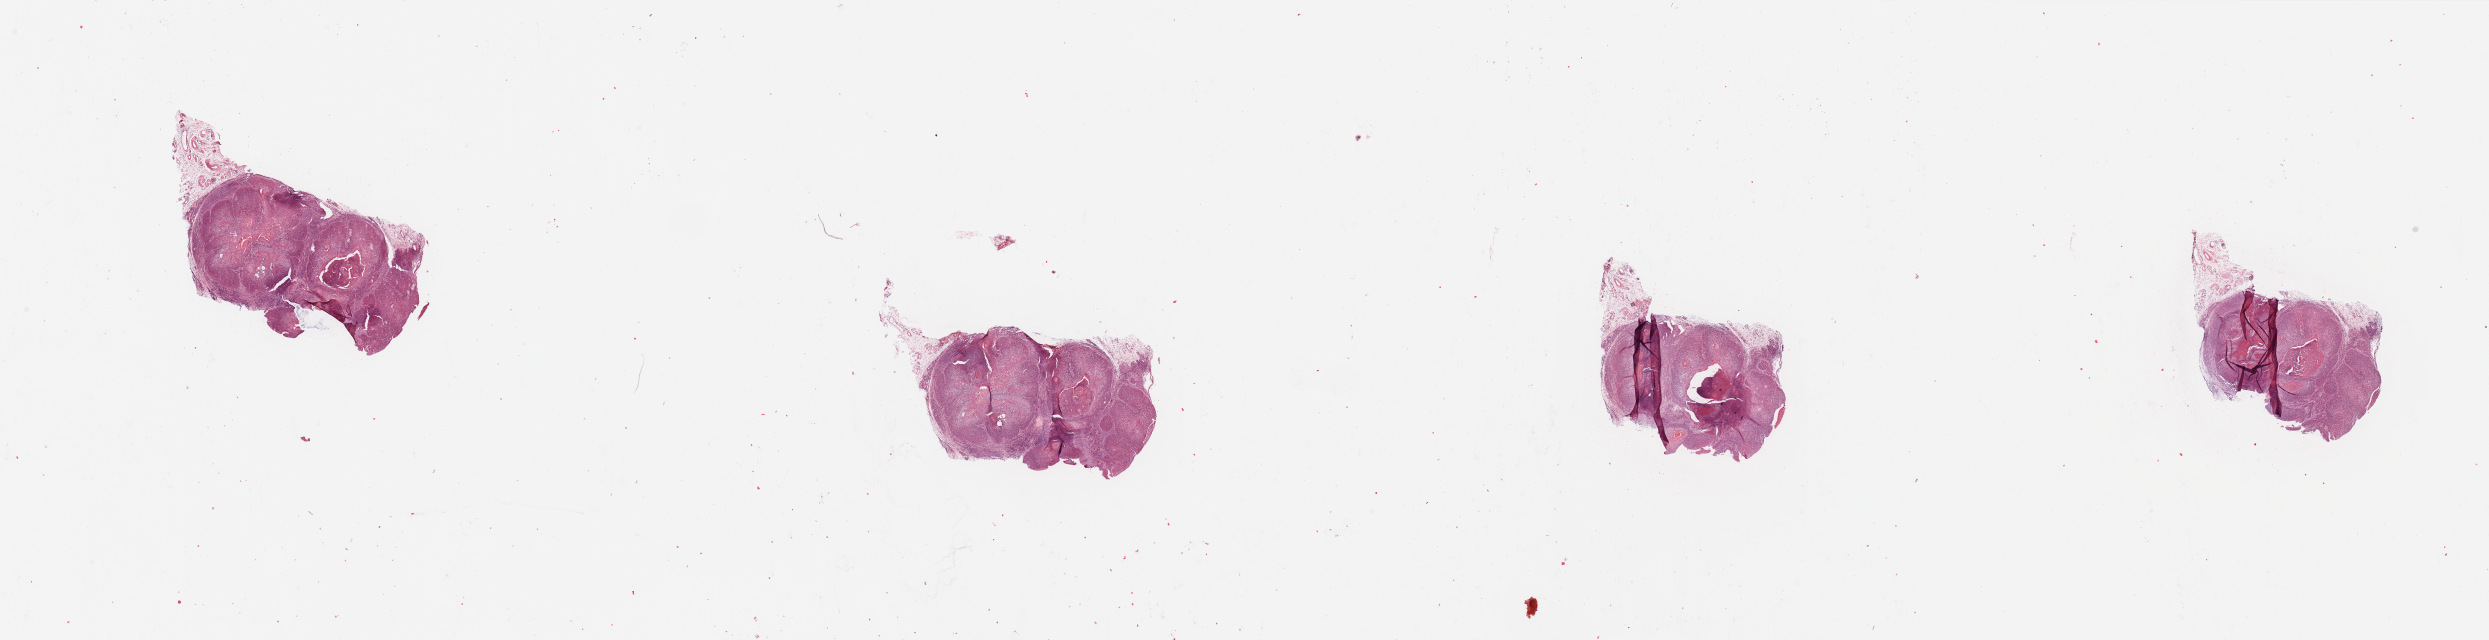
Digitized H&E-stained tissue section (whole slide), a low-resolution overview of the entire scanned area, about 39.4 x 10.1 mm (from a 20x scan); tumour tissue sample, sampled site: floor of mouth. Patient: male, age 65 years. Histologic grade: G2 (moderately differentiated). Pathologist review of this section (percent, as recorded): tumour nuclei 85%, necrosis 5%.
- AJCC pathologic stage: II
- primary tumour site (as recorded): oral cavity
- diagnosis: Squamous cell carcinoma, NOS (floor of mouth, NOS)